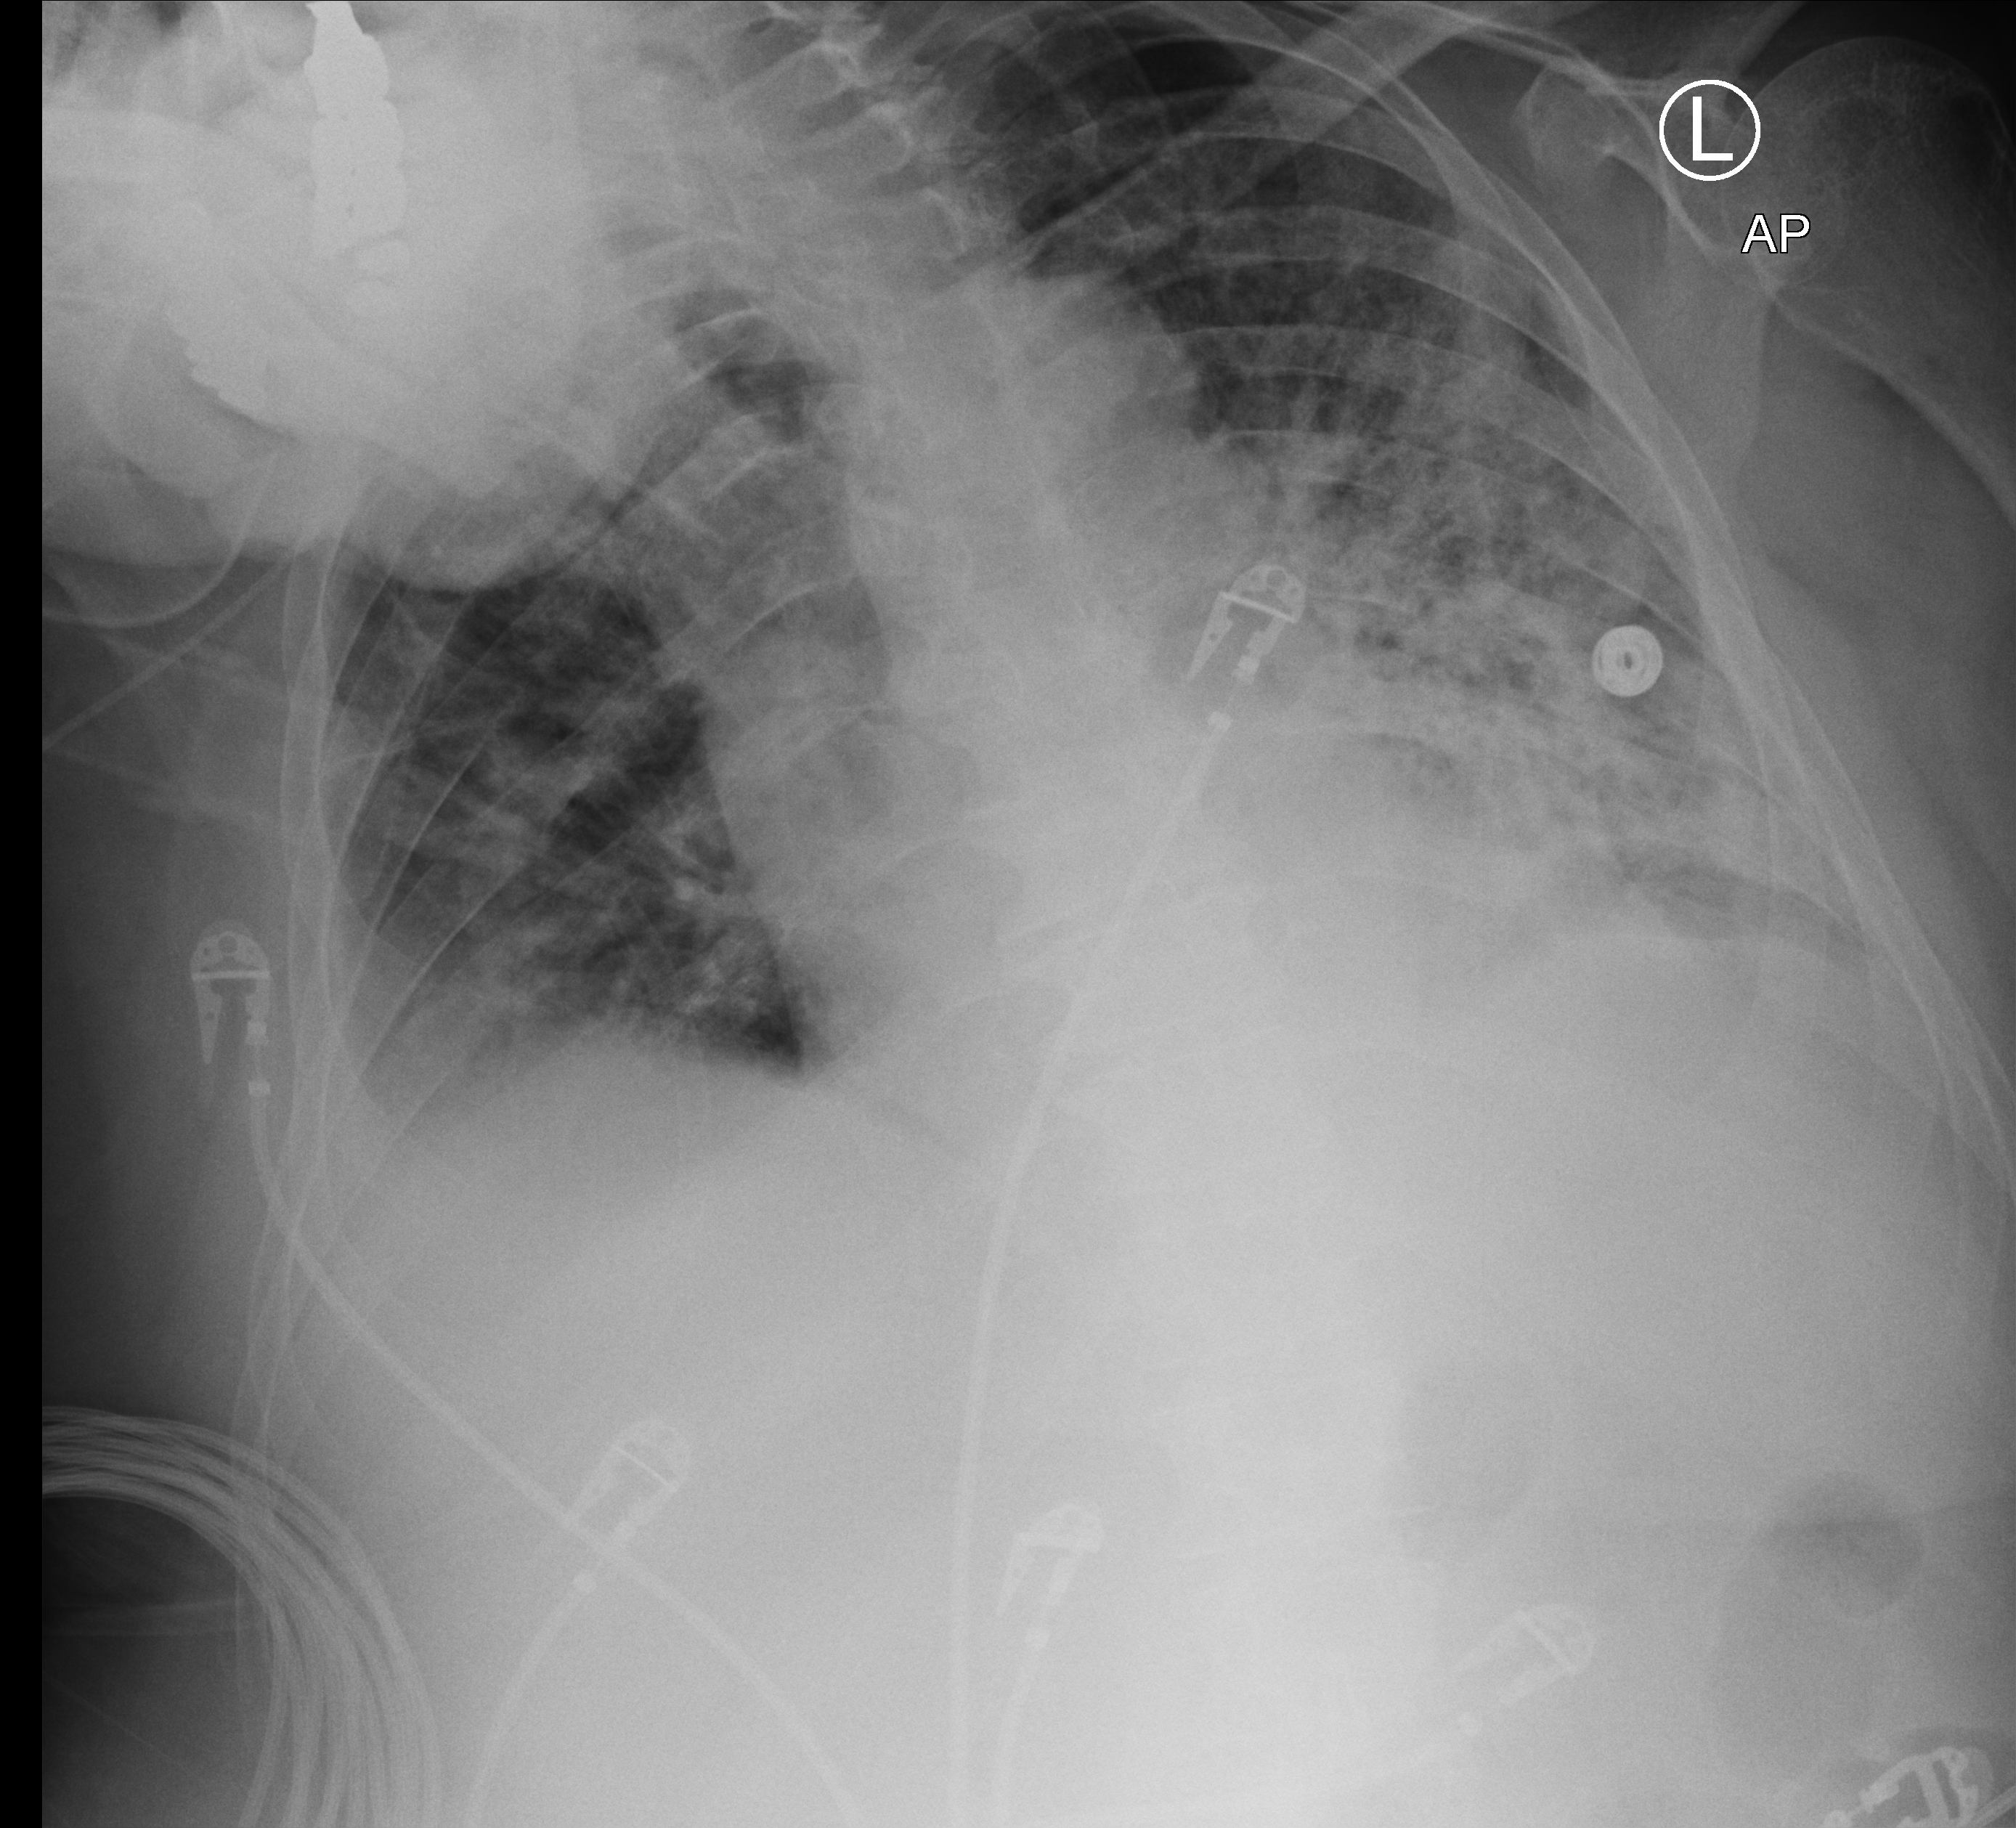
Bedside chest radiograph (computed radiography); anteroposterior (AP) projection. Male patient hospitalised with COVID-19, age 60–74 years.
Admission-level facts for this patient (not findings on this image; timing relative to this image not recorded): COPD (admission record): no.